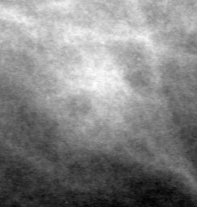
Crop from a digitized film mammogram around one marked abnormality, left breast, MLO view.
Marked abnormality: mass, shape lobulated, margins obscured; BI-RADS assessment category 0; subtlety rating 4 on a 1 (subtle) to 5 (obvious) scale; pathology (as recorded): malignant.